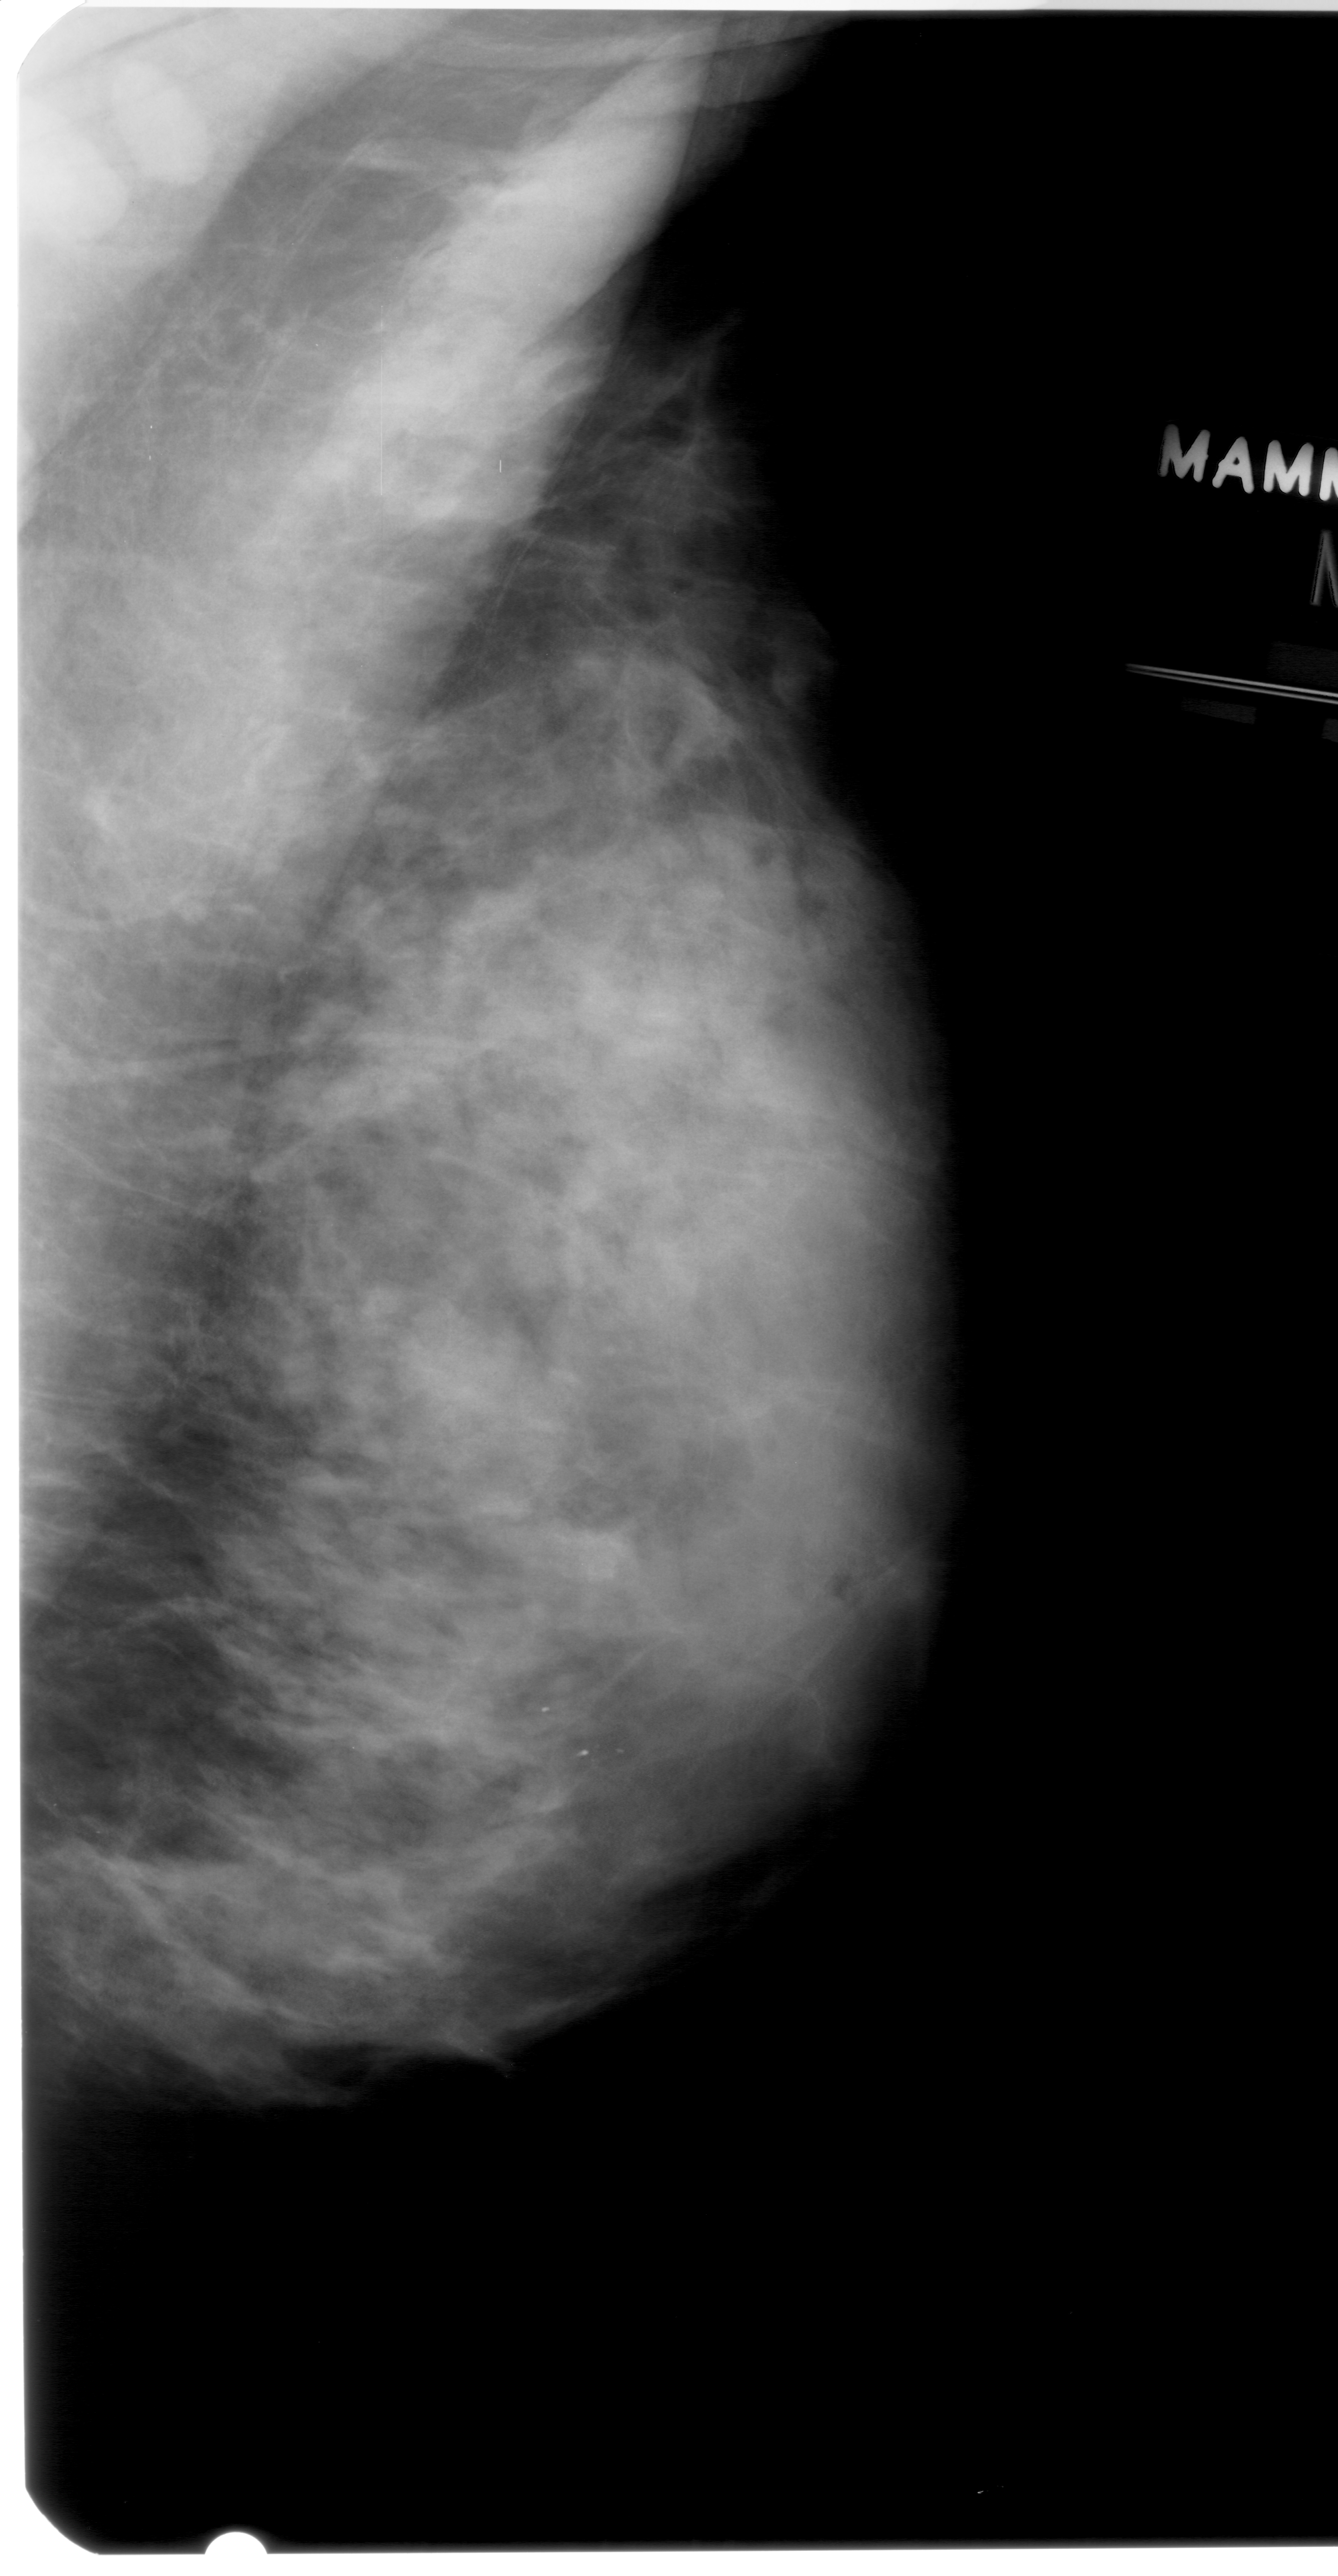
Mammogram (digitized film). Right breast. MLO view. Breast composition: extremely dense (BI-RADS density category 4 of 4). 1338 × 2576 image matrix.
Marked abnormalities (boxes around the expert regions of interest):
- calcifications, morphology pleomorphic, distribution clustered; BI-RADS assessment category 4; subtlety rating 4 on a 1 (subtle) to 5 (obvious) scale; pathology result (as recorded, not read from the image): benign: bounding box <477,1654,701,1860> (left, top, right, bottom; pixels)